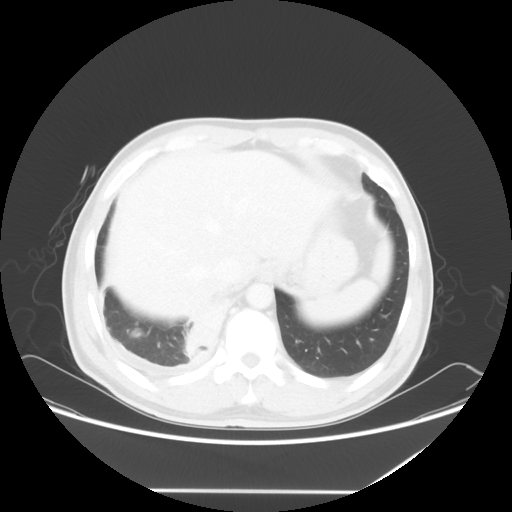
Chest CT, one axial slice. Slice 13 of 60 in the series (ordered by position). Lung window (W 1500 / L -600 HU). 5 mm slice thickness. 512 × 512 image matrix, field of view 419 × 419 mm. Male patient, age 48 years. Case-level facts recorded for this patient, not image findings: clinical TNM (as recorded): T3 N3 M1a.
Structures marked on this image (bounding box drawn by a radiologist):
- lung tumour (recorded histology: squamous cell carcinoma): bounding box (x1, y1, x2, y2) in pixels: (180, 294, 233, 364)